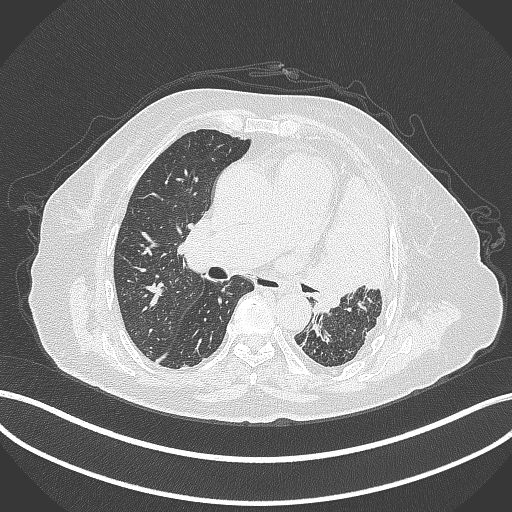
Chest CT, one axial slice; position 212 of 399 along the scan axis; lung window (W 1500 / L -600 HU); 1 mm slice thickness; 512 × 512 image matrix, field of view 400 × 400 mm. Patient: female, 75 years. From the clinical record (not read from this slice): clinical TNM (as recorded): T3 N3 M1.
Structures marked on this image (rectangle marked by the reading radiologist):
- lung tumour (recorded histology: adenocarcinoma): bounding box <308,169,396,323> (left, top, right, bottom; pixels)